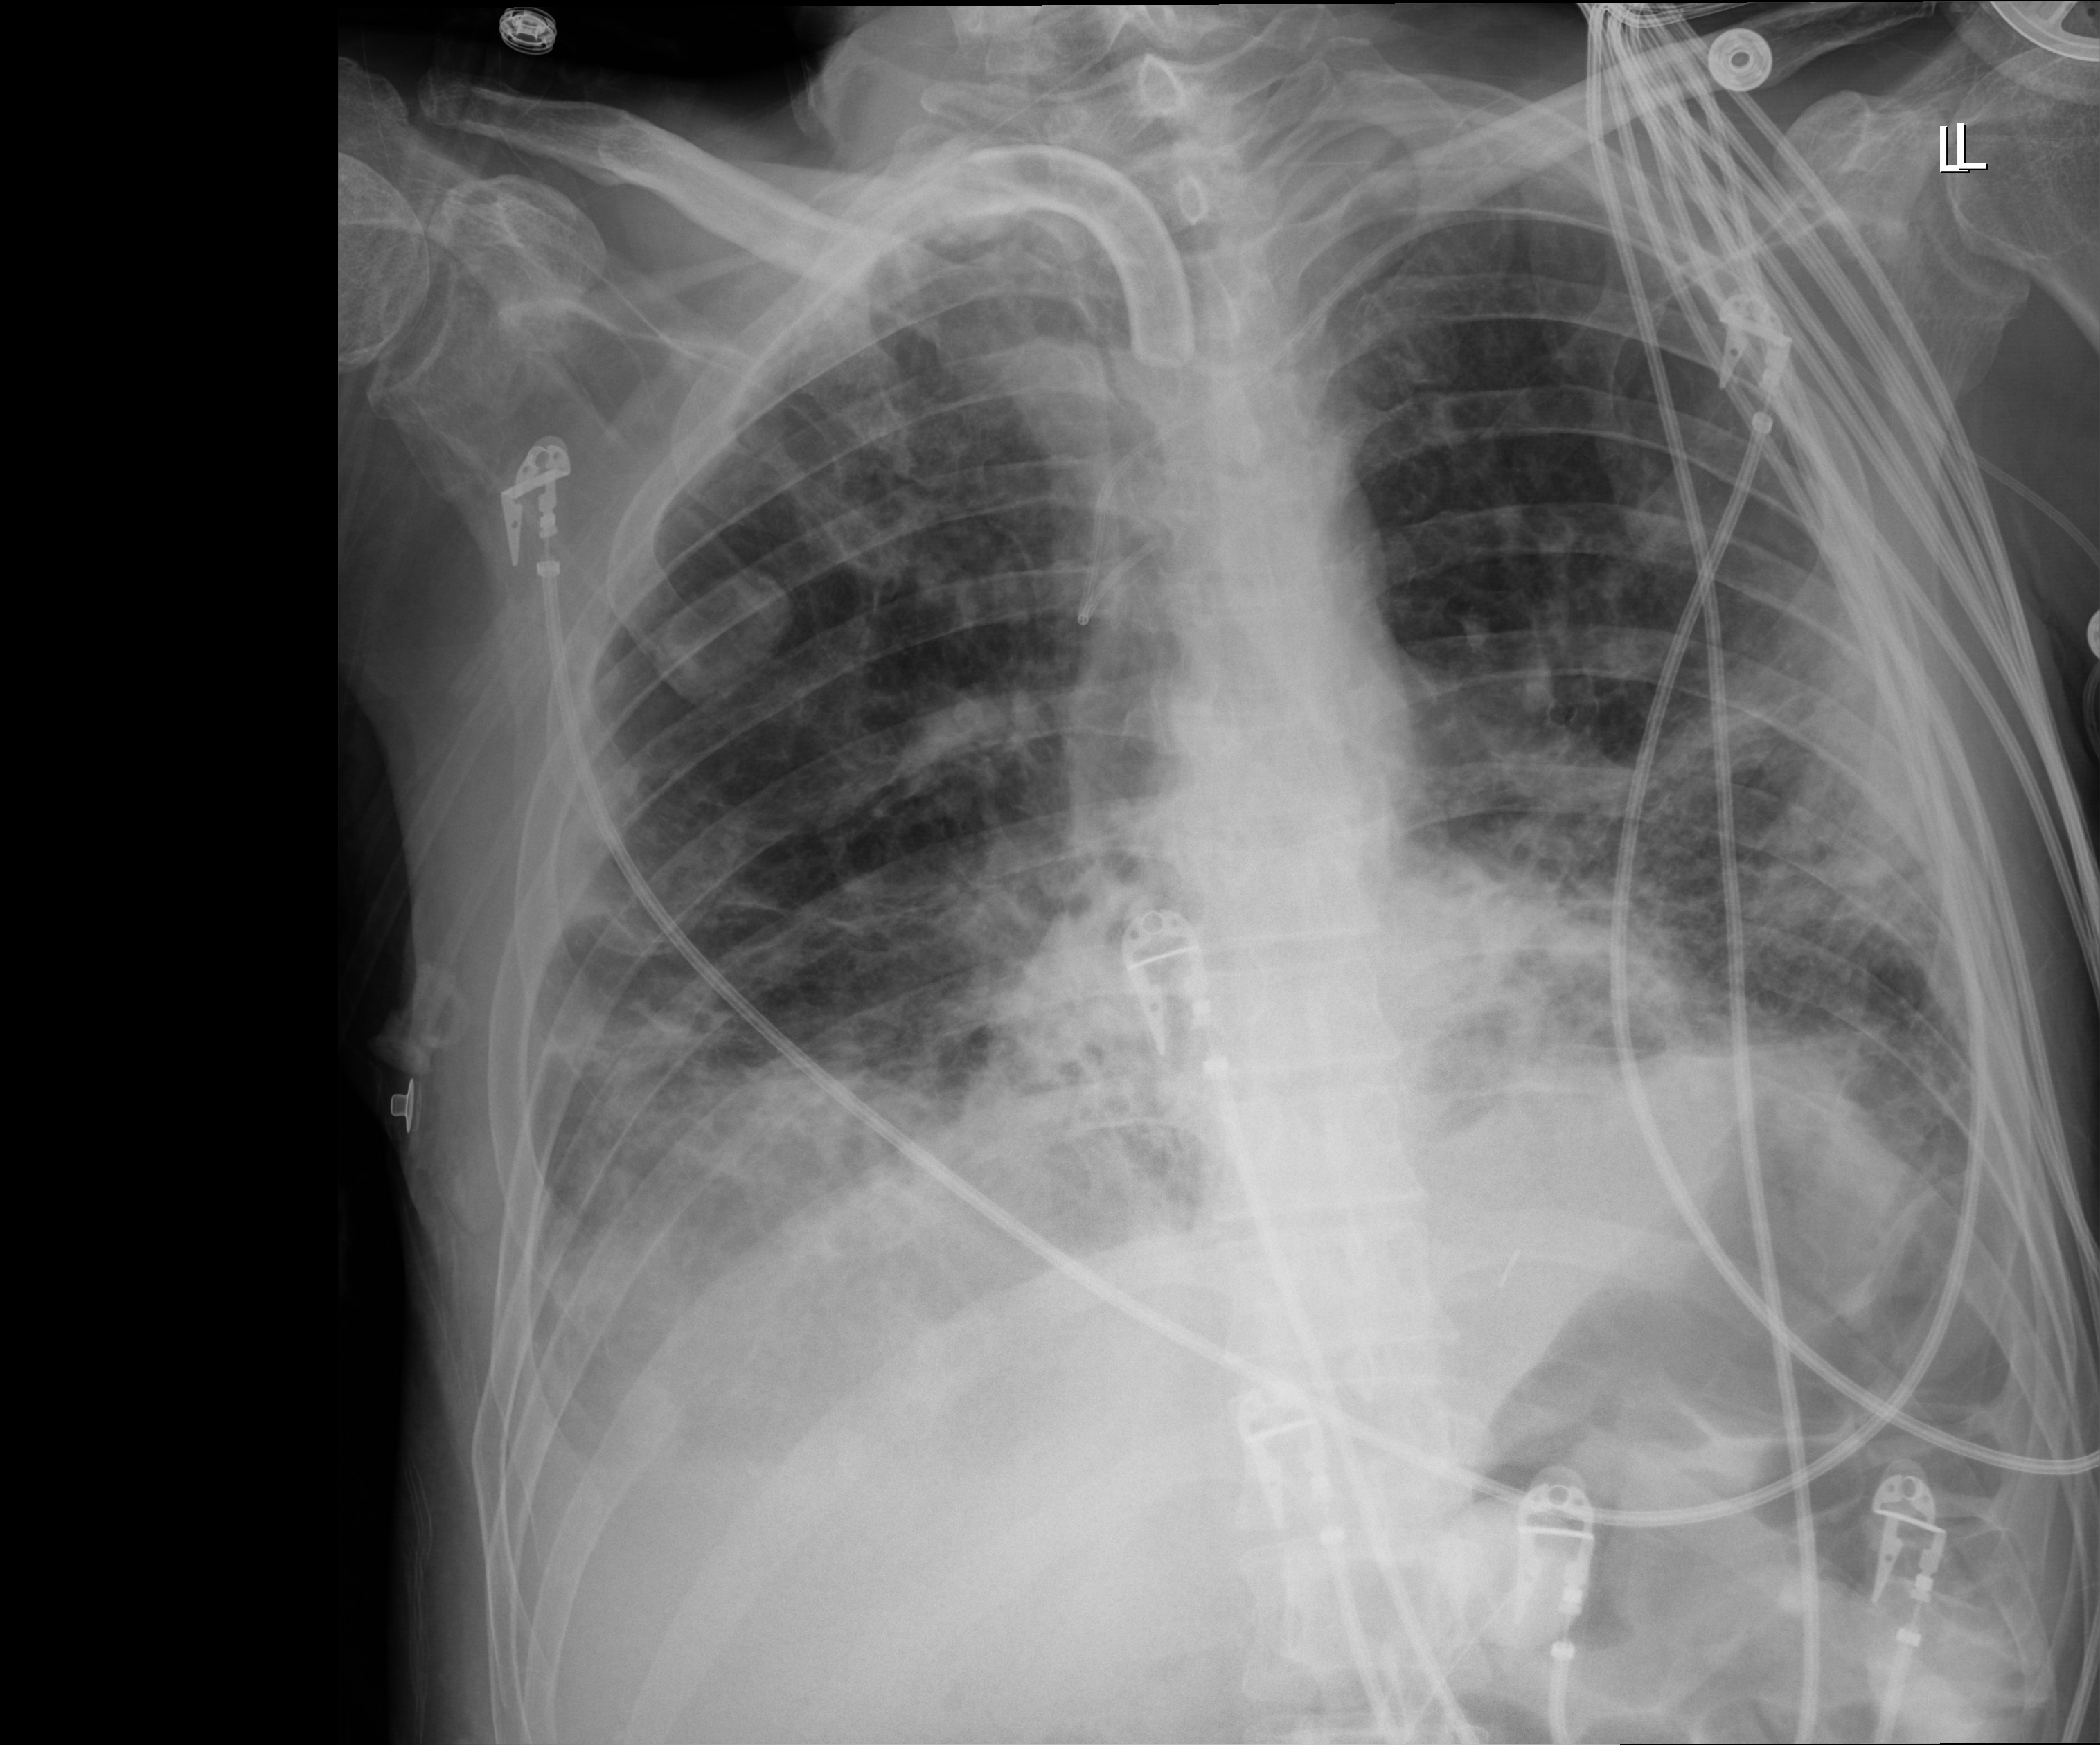
Chest X-ray, anteroposterior (AP) projection. Male patient hospitalised with COVID-19, age 18–59 years.
Admission-level facts for this patient (not findings on this image; timing relative to this image not recorded):
- mechanically ventilated during this hospital stay: yes
- admitted to intensive care during this hospital stay: yes
- smoking status (admission record): never